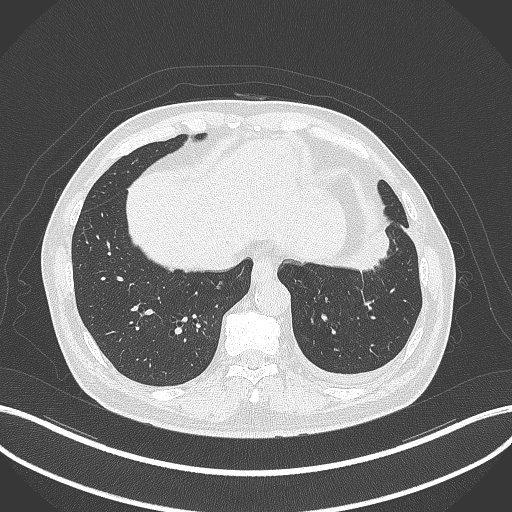
Chest CT, one axial slice; slice 86 of 230 in the series (ordered by position); 120 kVp; lung window (W 1500 / L -600 HU); 1 mm slice thickness; 512 × 512 image matrix, field of view 400 × 400 mm. Male patient, age 68 years. Case-level facts recorded for this patient, not image findings: clinical TNM (as recorded): T2b N0 M0.
Annotated regions visible in this slice (rectangle marked by the reading radiologist):
- lung tumour (recorded histology: squamous cell carcinoma): bounding box <344,228,394,278> (left, top, right, bottom; pixels)